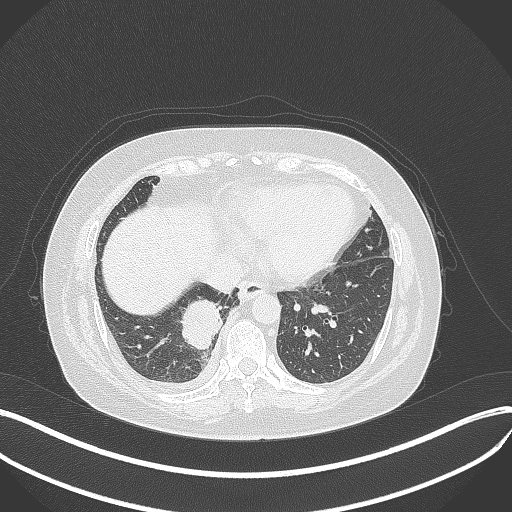
Chest CT, one axial slice. Slice 109 of 381 in the series (ordered by position). Reconstruction kernel B70f. 120 kVp. Lung window (W 1500 / L -600 HU). 1 mm slice thickness. 512 × 512 image matrix, field of view 400 × 400 mm. Female patient, age 56 years. Case-level facts recorded for this patient, not image findings: clinical TNM (as recorded): T2b N1 M0; histopathological grade: G3.
Structures marked on this image (rectangle marked by the reading radiologist):
- lung tumour (recorded histology: small cell carcinoma): bounding box [x1, y1, x2, y2] px = [182, 296, 229, 353]